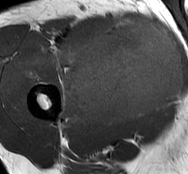
MRI of an extremity soft-tissue mass, one axial slice. Position 43 of 93 along the scan axis. MR volume resampled by the dataset authors to the PET/CT grid (not the native acquisition matrix). 188 × 174 image matrix, field of view 184 × 170 mm. Male patient. From the clinical record (not read from this slice): histological type: undifferentiated - pleiomorphic; grade: high; site of the primary tumour: right thigh.
Outlined on this slice (expert contour drawn on MRI and transferred to this co-registered scan by the dataset authors):
- gross tumour volume including surrounding oedema: bounding box [x1, y1, x2, y2] px = [58, 19, 183, 127]
- gross tumour volume (mass): [70, 19, 183, 123]